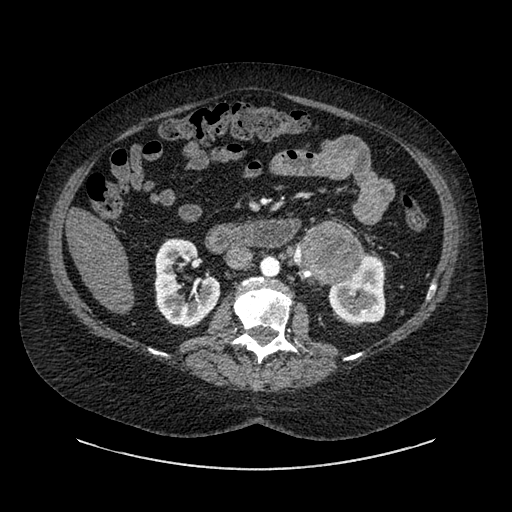
Contrast-enhanced abdominal CT, one axial slice. Position 503 of 769 along the scan axis. 120 kVp. Intravenous contrast given. Soft-tissue window (W 400 / L 40 HU). 0.62 mm slice thickness. 512 × 512 image matrix, field of view 460 × 460 mm. Female patient, age 61 years. Case-level facts recorded for this patient, not image findings: diagnosis: adrenocortical carcinoma; tumour side: left adrenal.
Annotated regions visible in this slice (semi-automatic segmentation, software-assisted and operator-edited):
- mass: box from (x=296, y=225) to (x=360, y=282) px